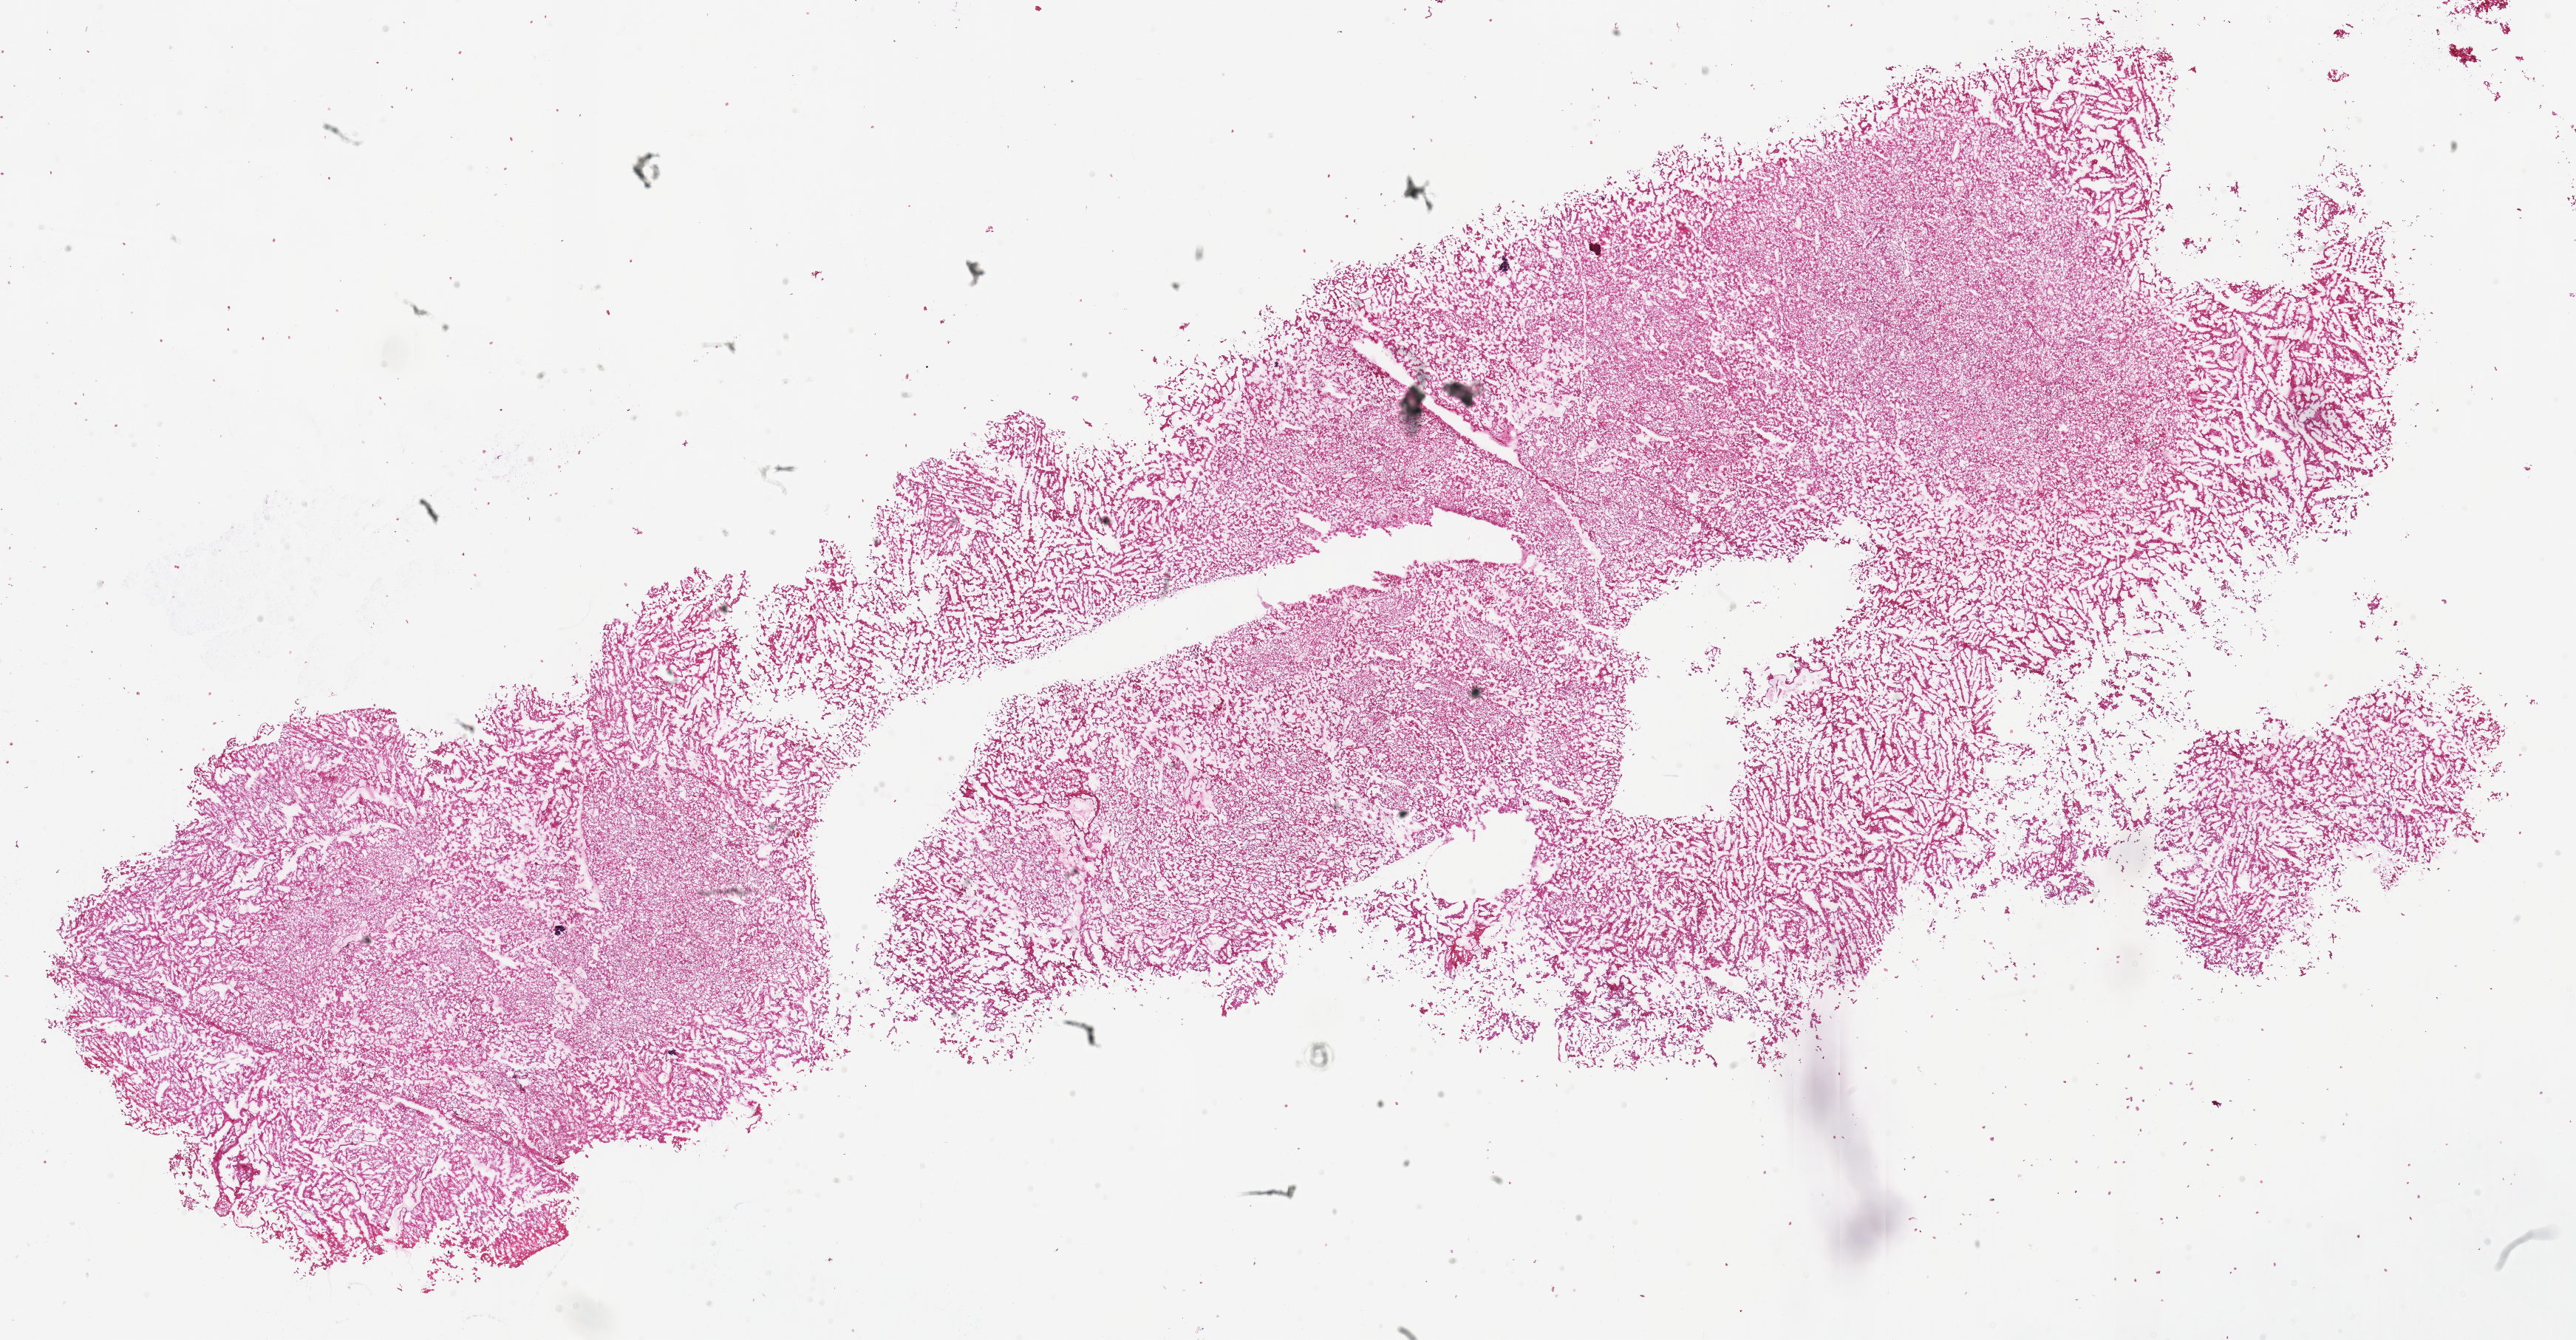
H&E whole-slide image, whole scanned area (about 27.4 x 14.3 mm) shown as a low-resolution overview. Frozen section from the top of the tissue portion. Kidney, primary tumour sample. Male patient; age at initial diagnosis 47 years. Pathologist review of this section (percent, as recorded): tumour cells 90%, tumour nuclei 90%, normal cells 0%, stromal cells 10%, necrosis 0%.
AJCC pathologic stage: III (7th edition). Pathologic diagnosis: Renal cell carcinoma, chromophobe type.